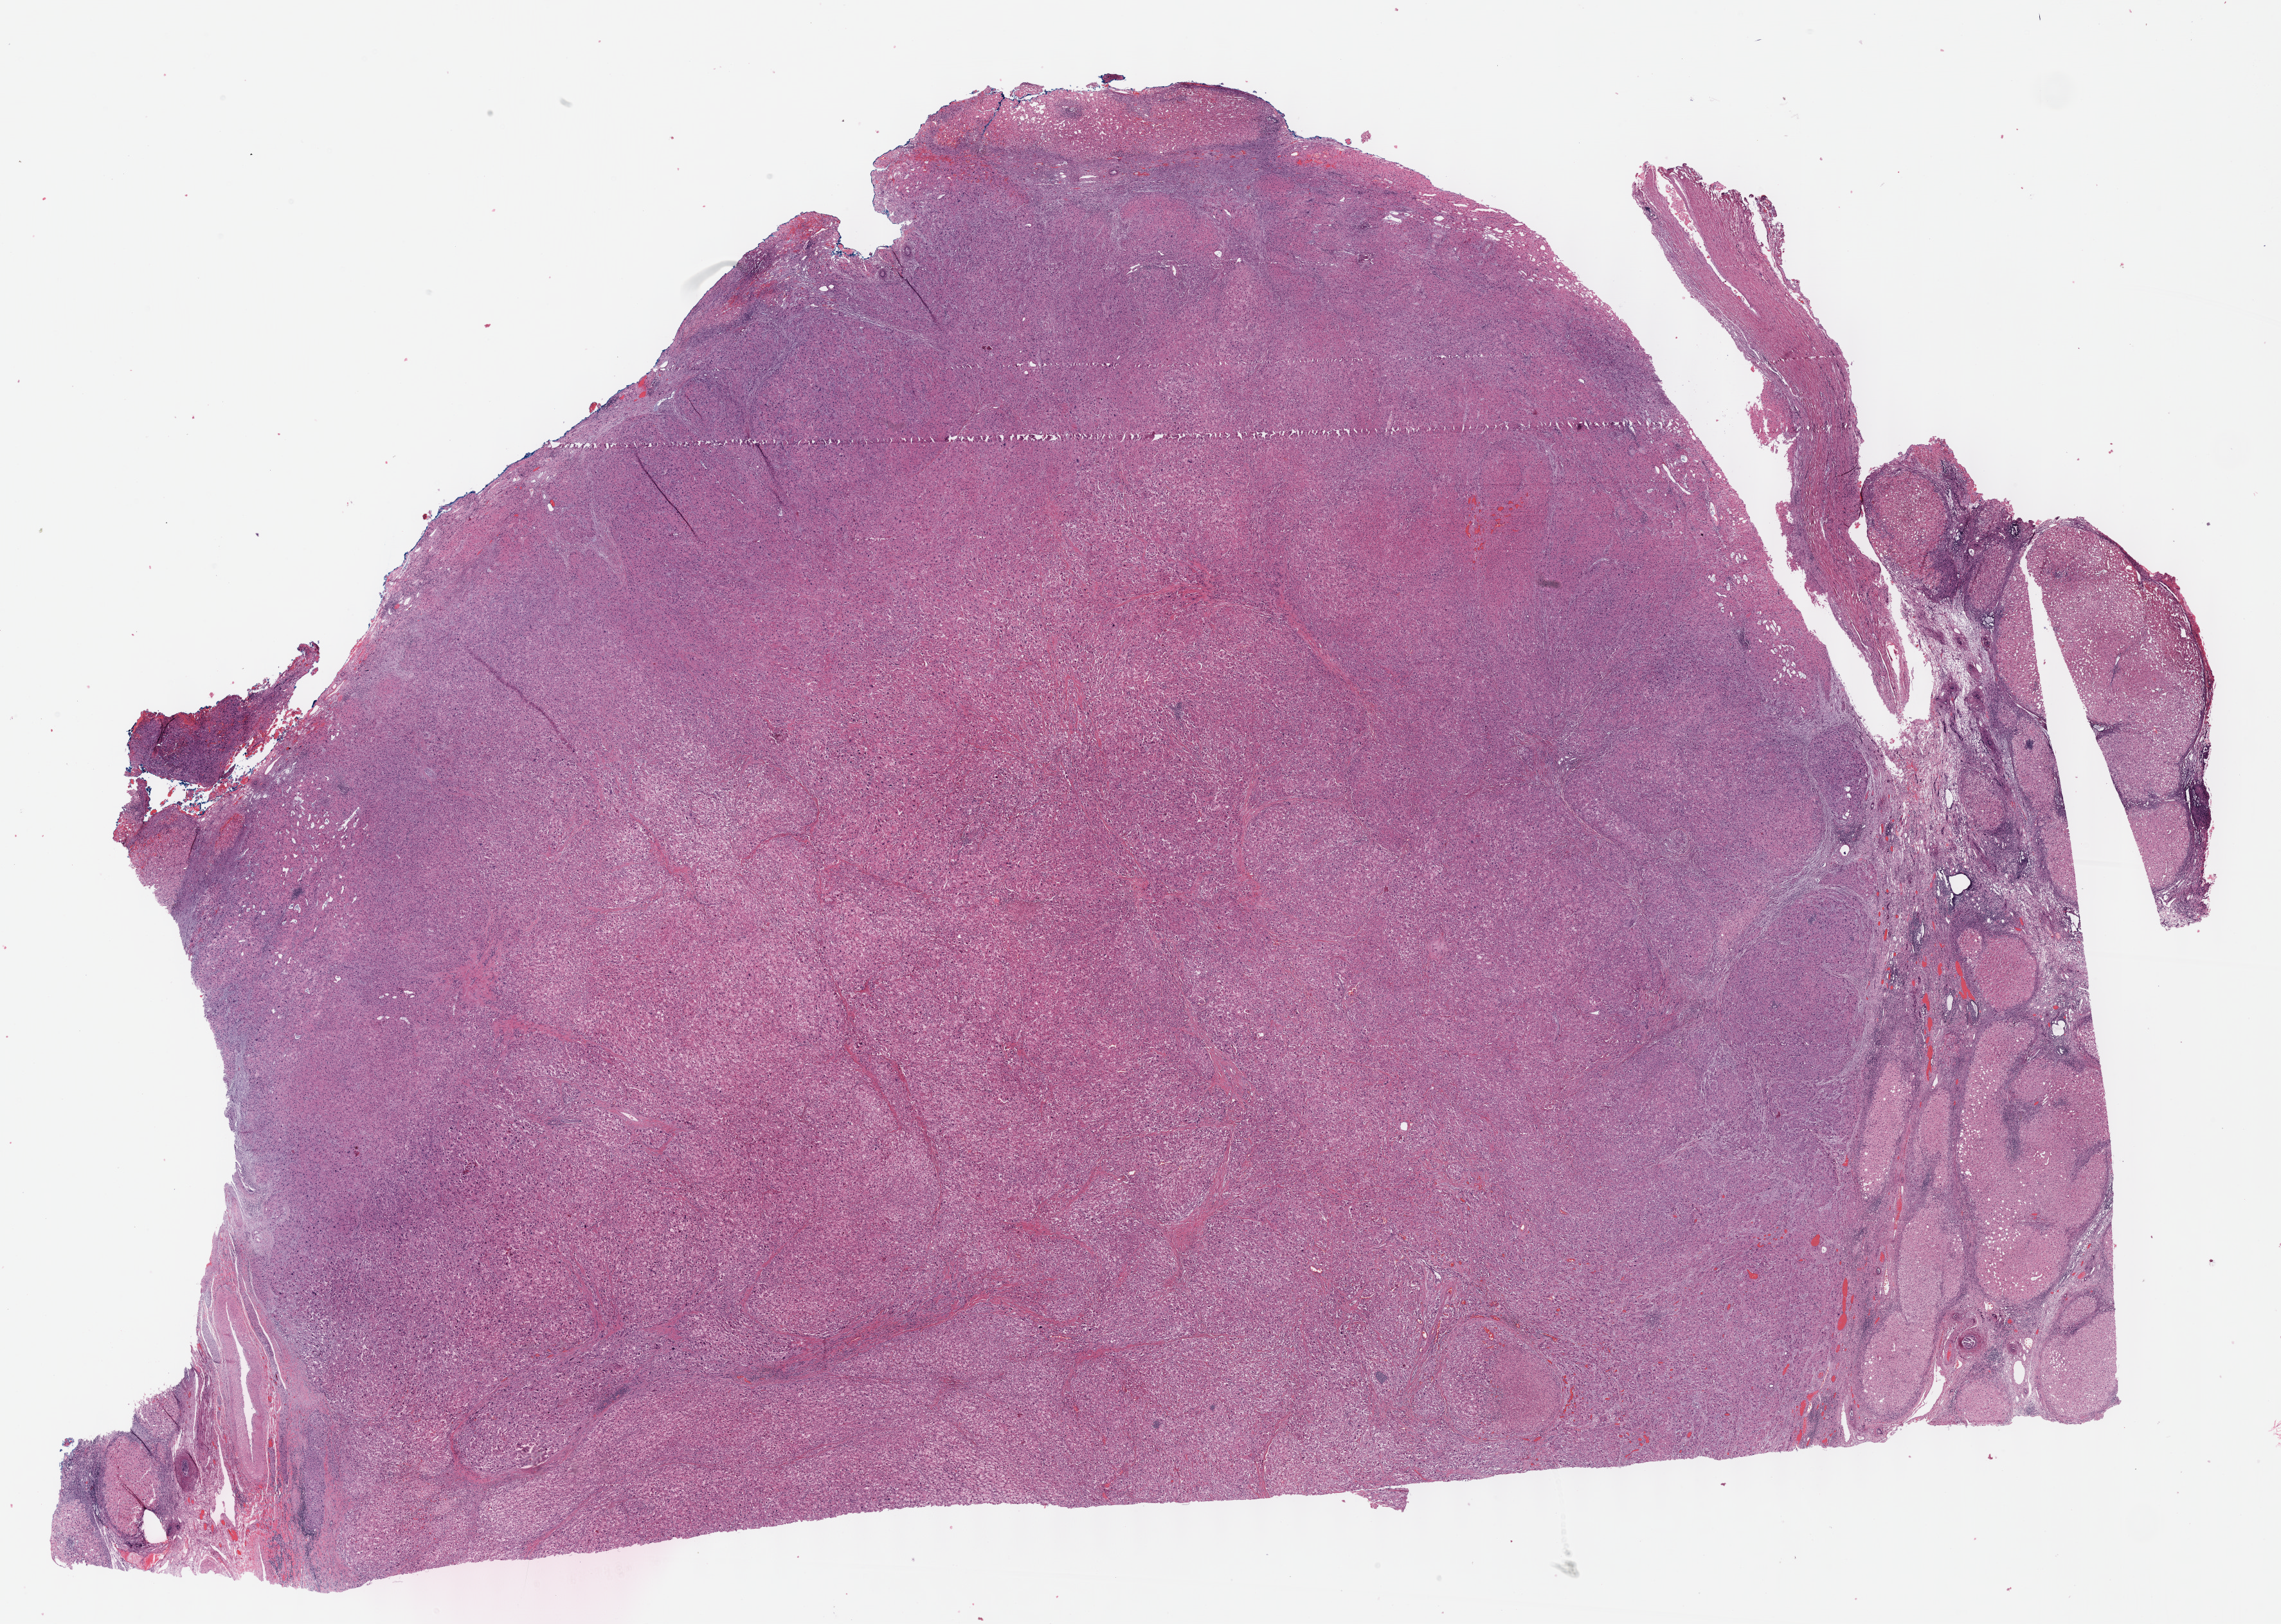
Hematoxylin and eosin (H&E) stained whole-slide image — shown as a low-resolution overview of the whole scanned area (about 28.7 x 20.4 mm, acquisition: 40x scan); FFPE section; liver, primary tumour sample. Patient: male, age at initial diagnosis 58 years. Histologic grade: G3 (poorly differentiated).
* histologic diagnosis: Hepatocellular carcinoma, NOS
* TNM: T2 NX M0
* AJCC pathologic stage: II